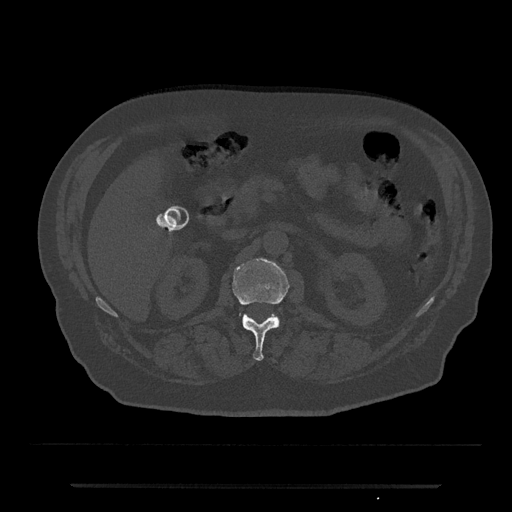
CT including the spine, one axial slice. Position 525 of 797 along the scan axis. Reconstruction kernel Br40s/3. Bone window (W 1800 / L 400 HU). 0.5 mm slice thickness. 512 × 512 image matrix, field of view 434 × 434 mm. Male patient, age 80 years. Case-level facts recorded for this patient, not image findings: primary cancer: prostate.
Annotated regions visible in this slice (semi-automatically segmented with operator editing):
- L1 vertebra: bounding box [x1, y1, x2, y2] px = [232, 259, 290, 361]